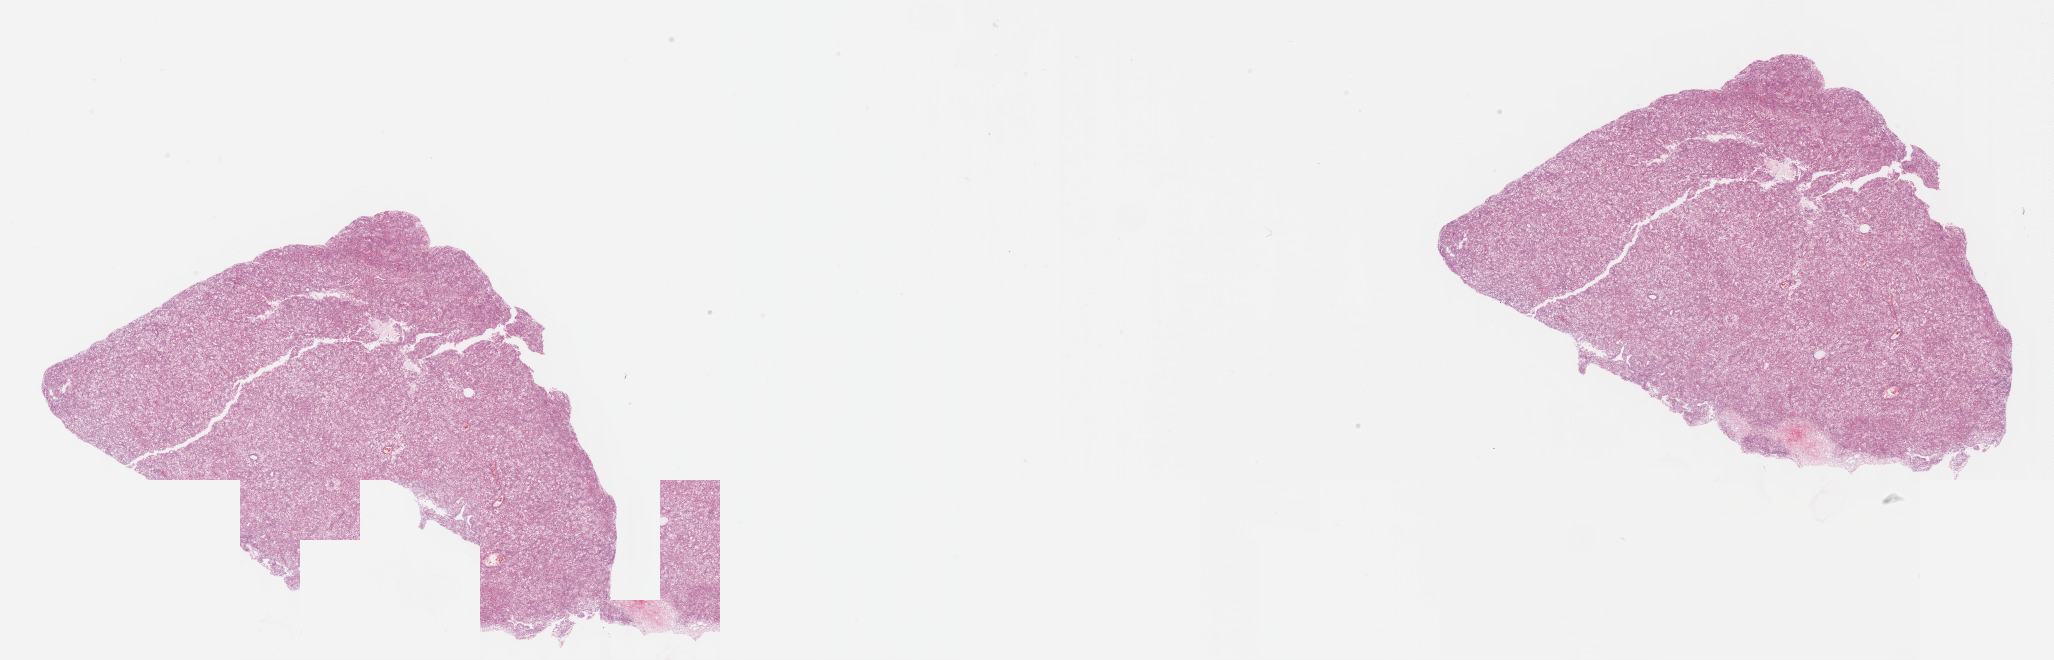
Whole-slide histology image, H&E — low-resolution overview of the scanned area, about 33.2 x 10.7 mm (acquisition: 40x scan). Formalin-fixed paraffin-embedded (FFPE) diagnostic section. Liver, primary tumour sample. Male patient; age at initial diagnosis 70 years. Histologic grade: G2 (moderately differentiated).
- histologic diagnosis: Hepatocellular carcinoma, NOS
- AJCC pathologic stage: I (6th edition)